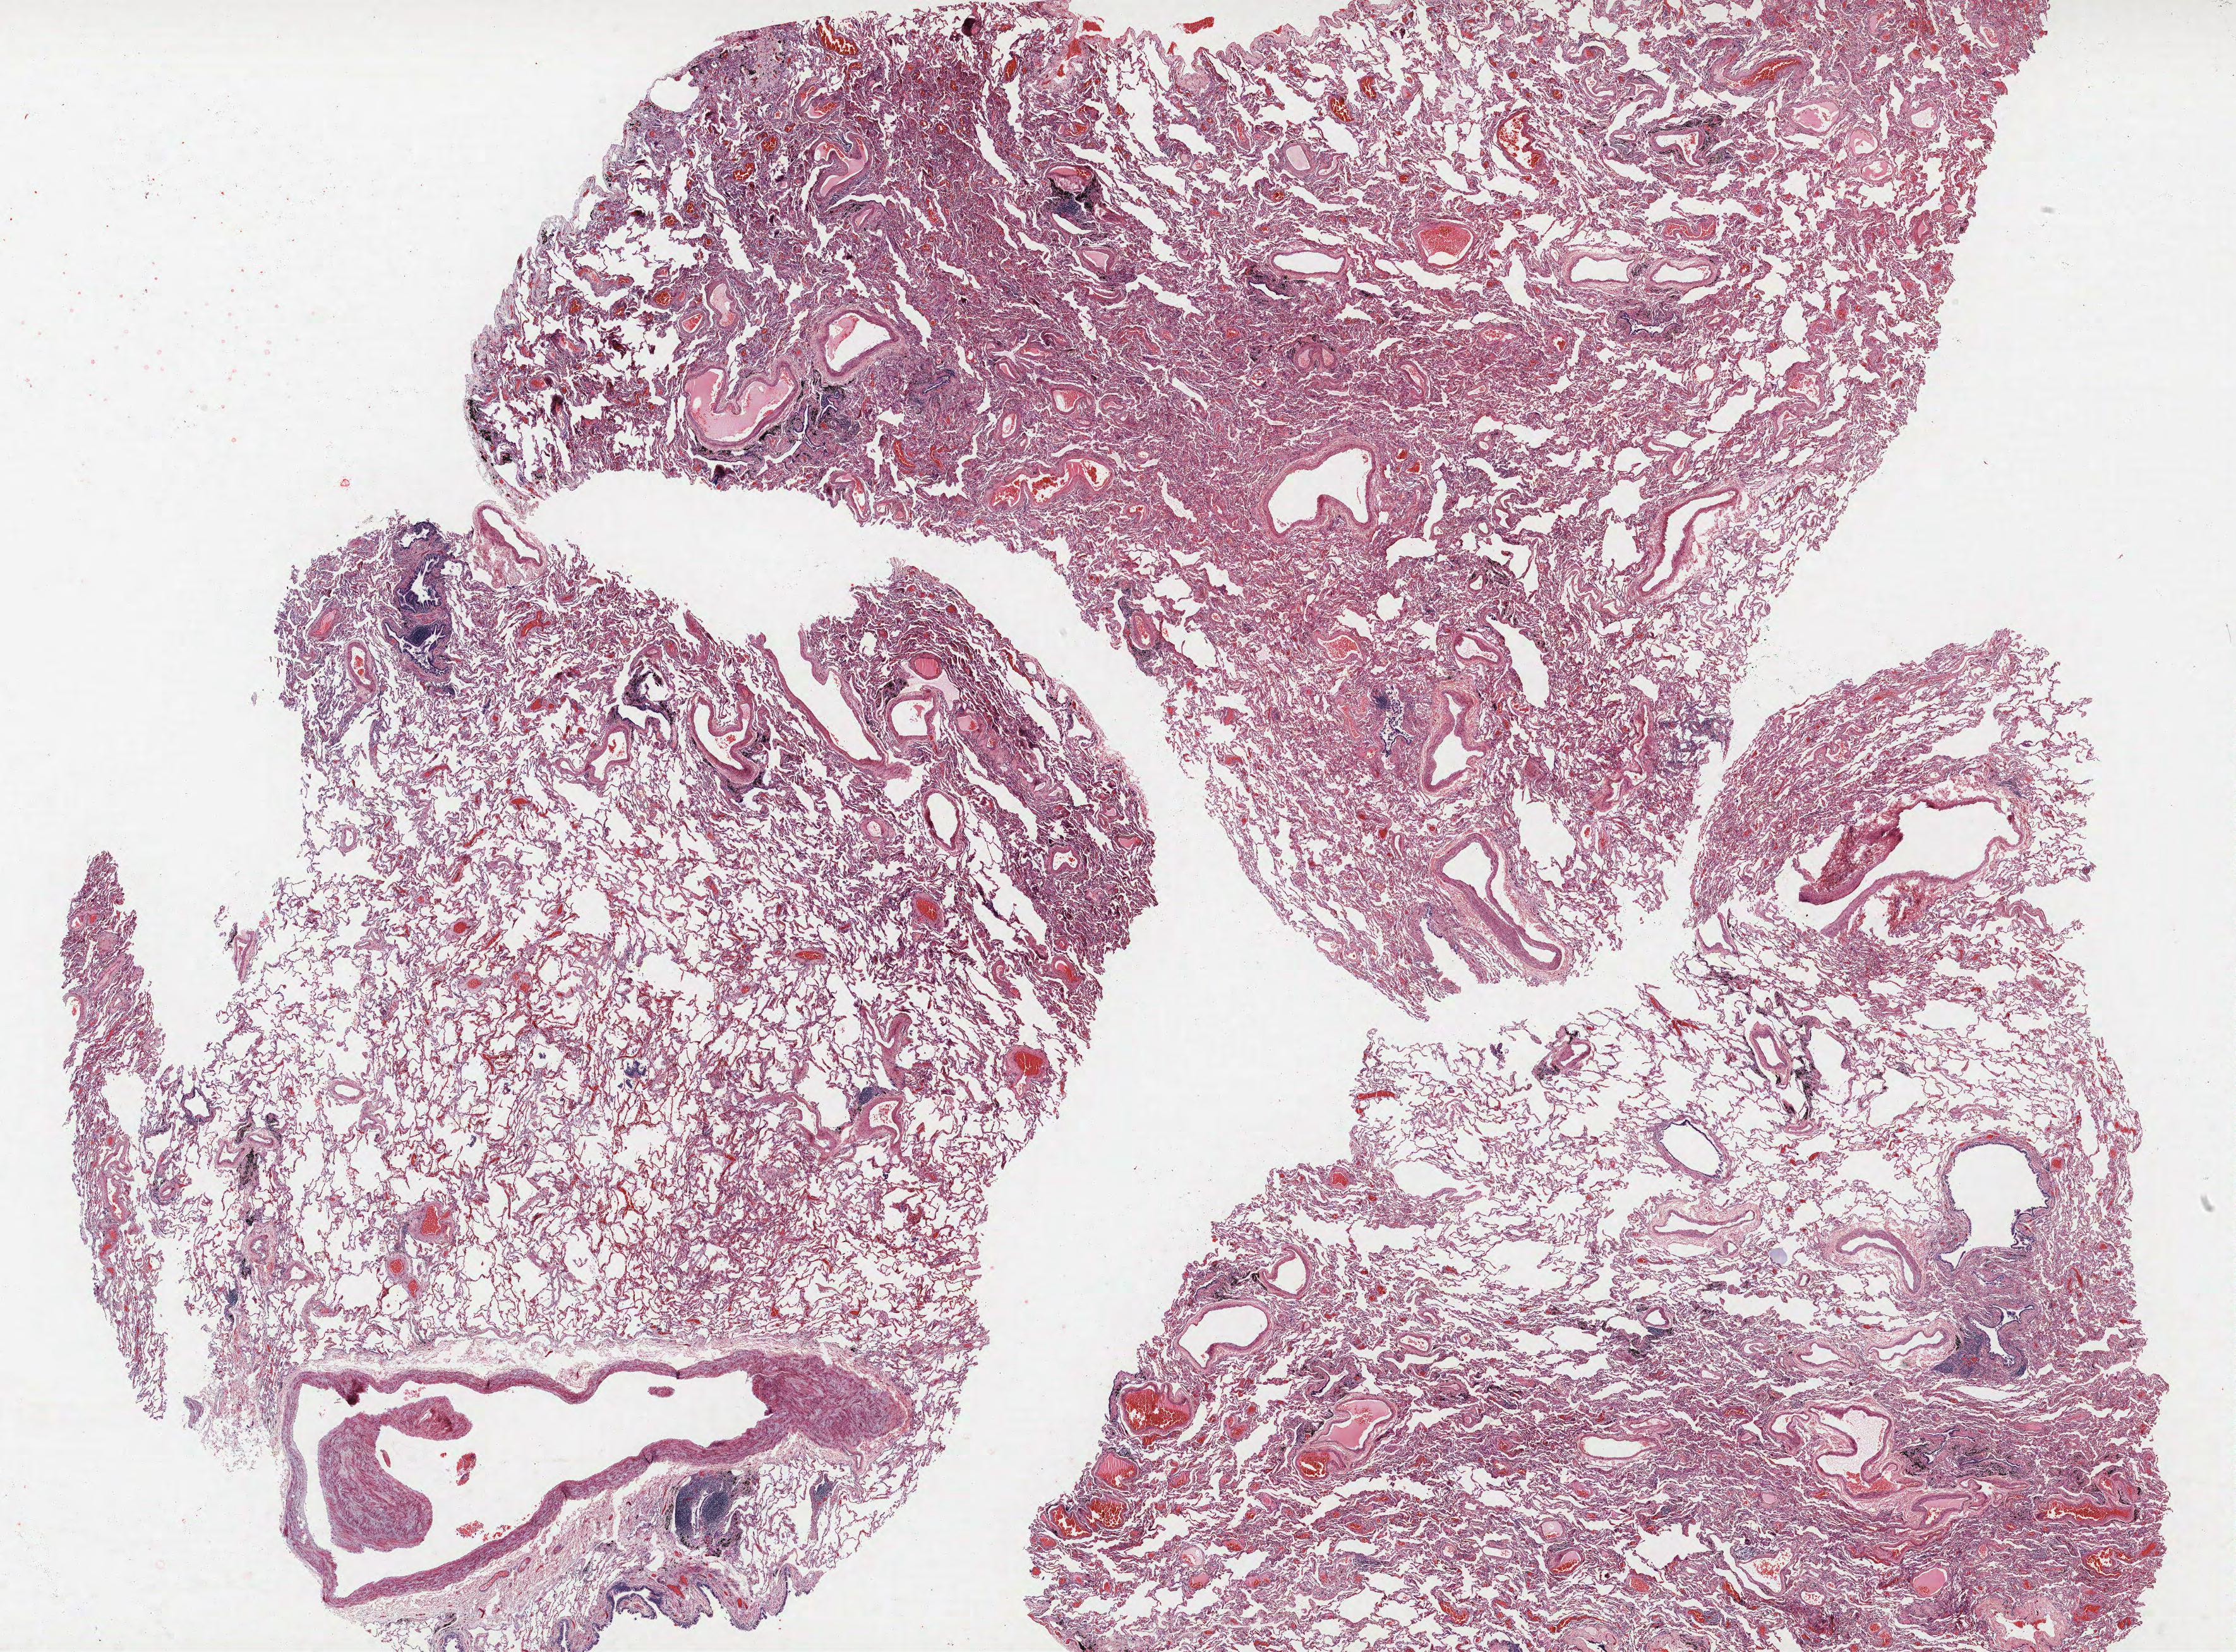
Whole-slide histology image, H&E — a low-resolution overview of the entire scanned area, about 28.3 x 20.9 mm (slide scanned at 40x); formalin-fixed paraffin-embedded (FFPE) section; lung tissue. Male patient, aged 74 at enrolment. Former smoker at enrolment. Grade: poorly differentiated (G3).
Primary tumour location (clinical record): left upper lobe. Participant's lung-cancer diagnosis: Adenocarcinoma, NOS (ICD-O-3 8140/3). Tumour size (pathology): 27 mm. Stage (AJCC 6th edition): IIIA.